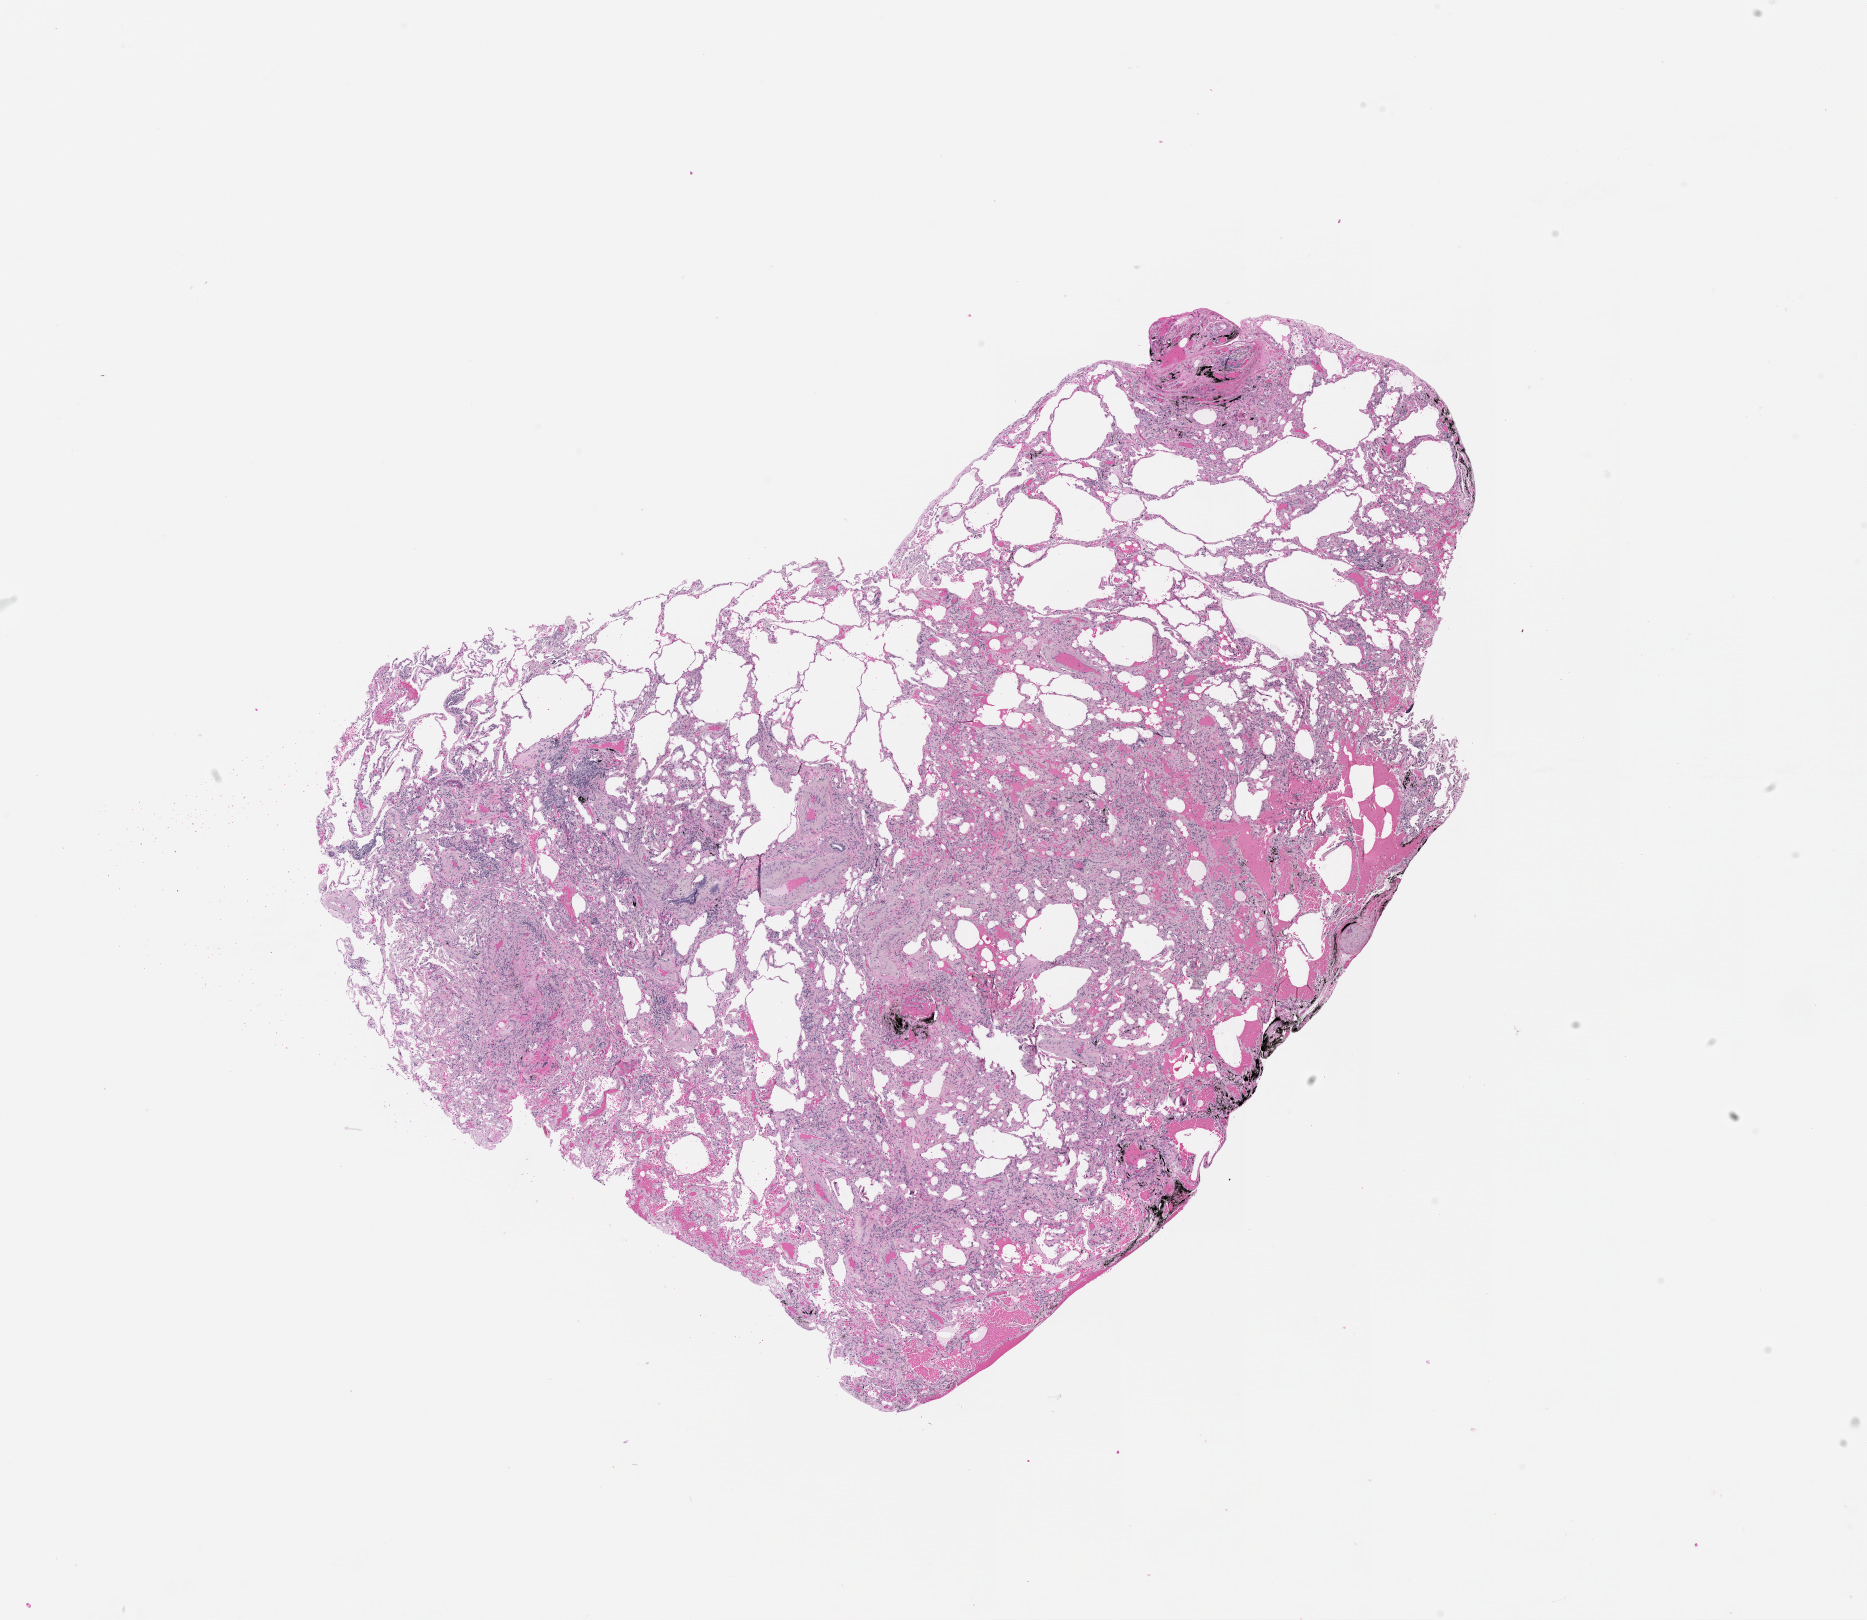
Whole-slide histology image, H&E — low-resolution overview of the scanned area, about 15.0 x 13.0 mm (from a 20x scan). Normal (non-tumour) tissue sample, lung. Female patient.
* this section: normal (non-tumour) tissue from the same patient
* patient diagnosis (cohort enrolment): squamous cell carcinoma (lung)